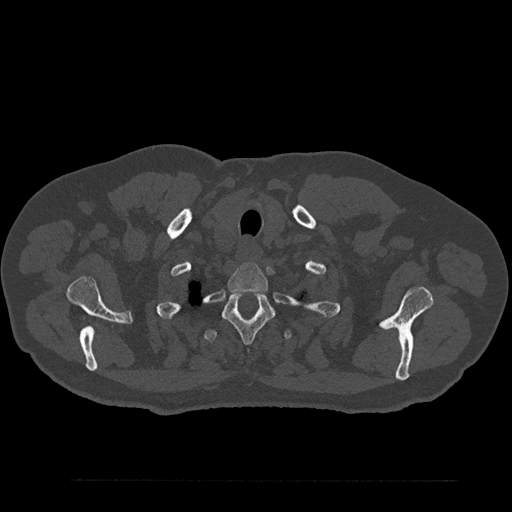
CT including the spine, one axial slice; slice 721 of 797 in the series (ordered by position); reconstruction kernel Br40s/3; 120 kVp; bone window (W 1800 / L 400 HU); 0.5 mm slice thickness; 512 × 512 image matrix, field of view 430 × 430 mm. Male patient, age 61 years. Case-level facts recorded for this patient, not image findings: primary cancer: prostate.
Annotated regions visible in this slice (semi-automatic segmentation, software-assisted and operator-edited):
- T1 vertebra: bounding box <227,263,268,293> (left, top, right, bottom; pixels)
- T2 vertebra: <223,292,274,344>
- T3 vertebra: <204,329,293,343>